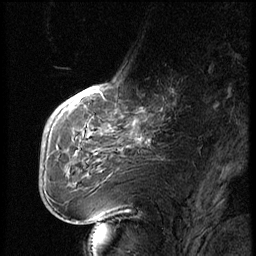
Breast MRI (dynamic contrast-enhanced), one sagittal slice; slice 22 of 74 in the series (ordered by position); dynamic contrast-enhanced series, image 2 of 3 at this slice position (ordered by acquisition); 1.5 T; TE 4.2 ms, TR 9 ms; 2.5 mm slice thickness; 256 × 256 image matrix. Patient: female, 56 years. Case-level facts recorded for this patient, not image findings: setting: breast cancer imaged before/during neoadjuvant chemotherapy.
Outlined on this slice (semi-automatic segmentation, software-assisted and operator-edited):
- analysis volume of interest (the breast-tissue region the enhancement analysis was run in; not a lesion): bounding box [x1, y1, x2, y2] px = [123, 71, 195, 131]
- tumour enhancement mask (voxels above the 140 % enhancement threshold inside the analysis volume of interest): [172, 91, 174, 93]